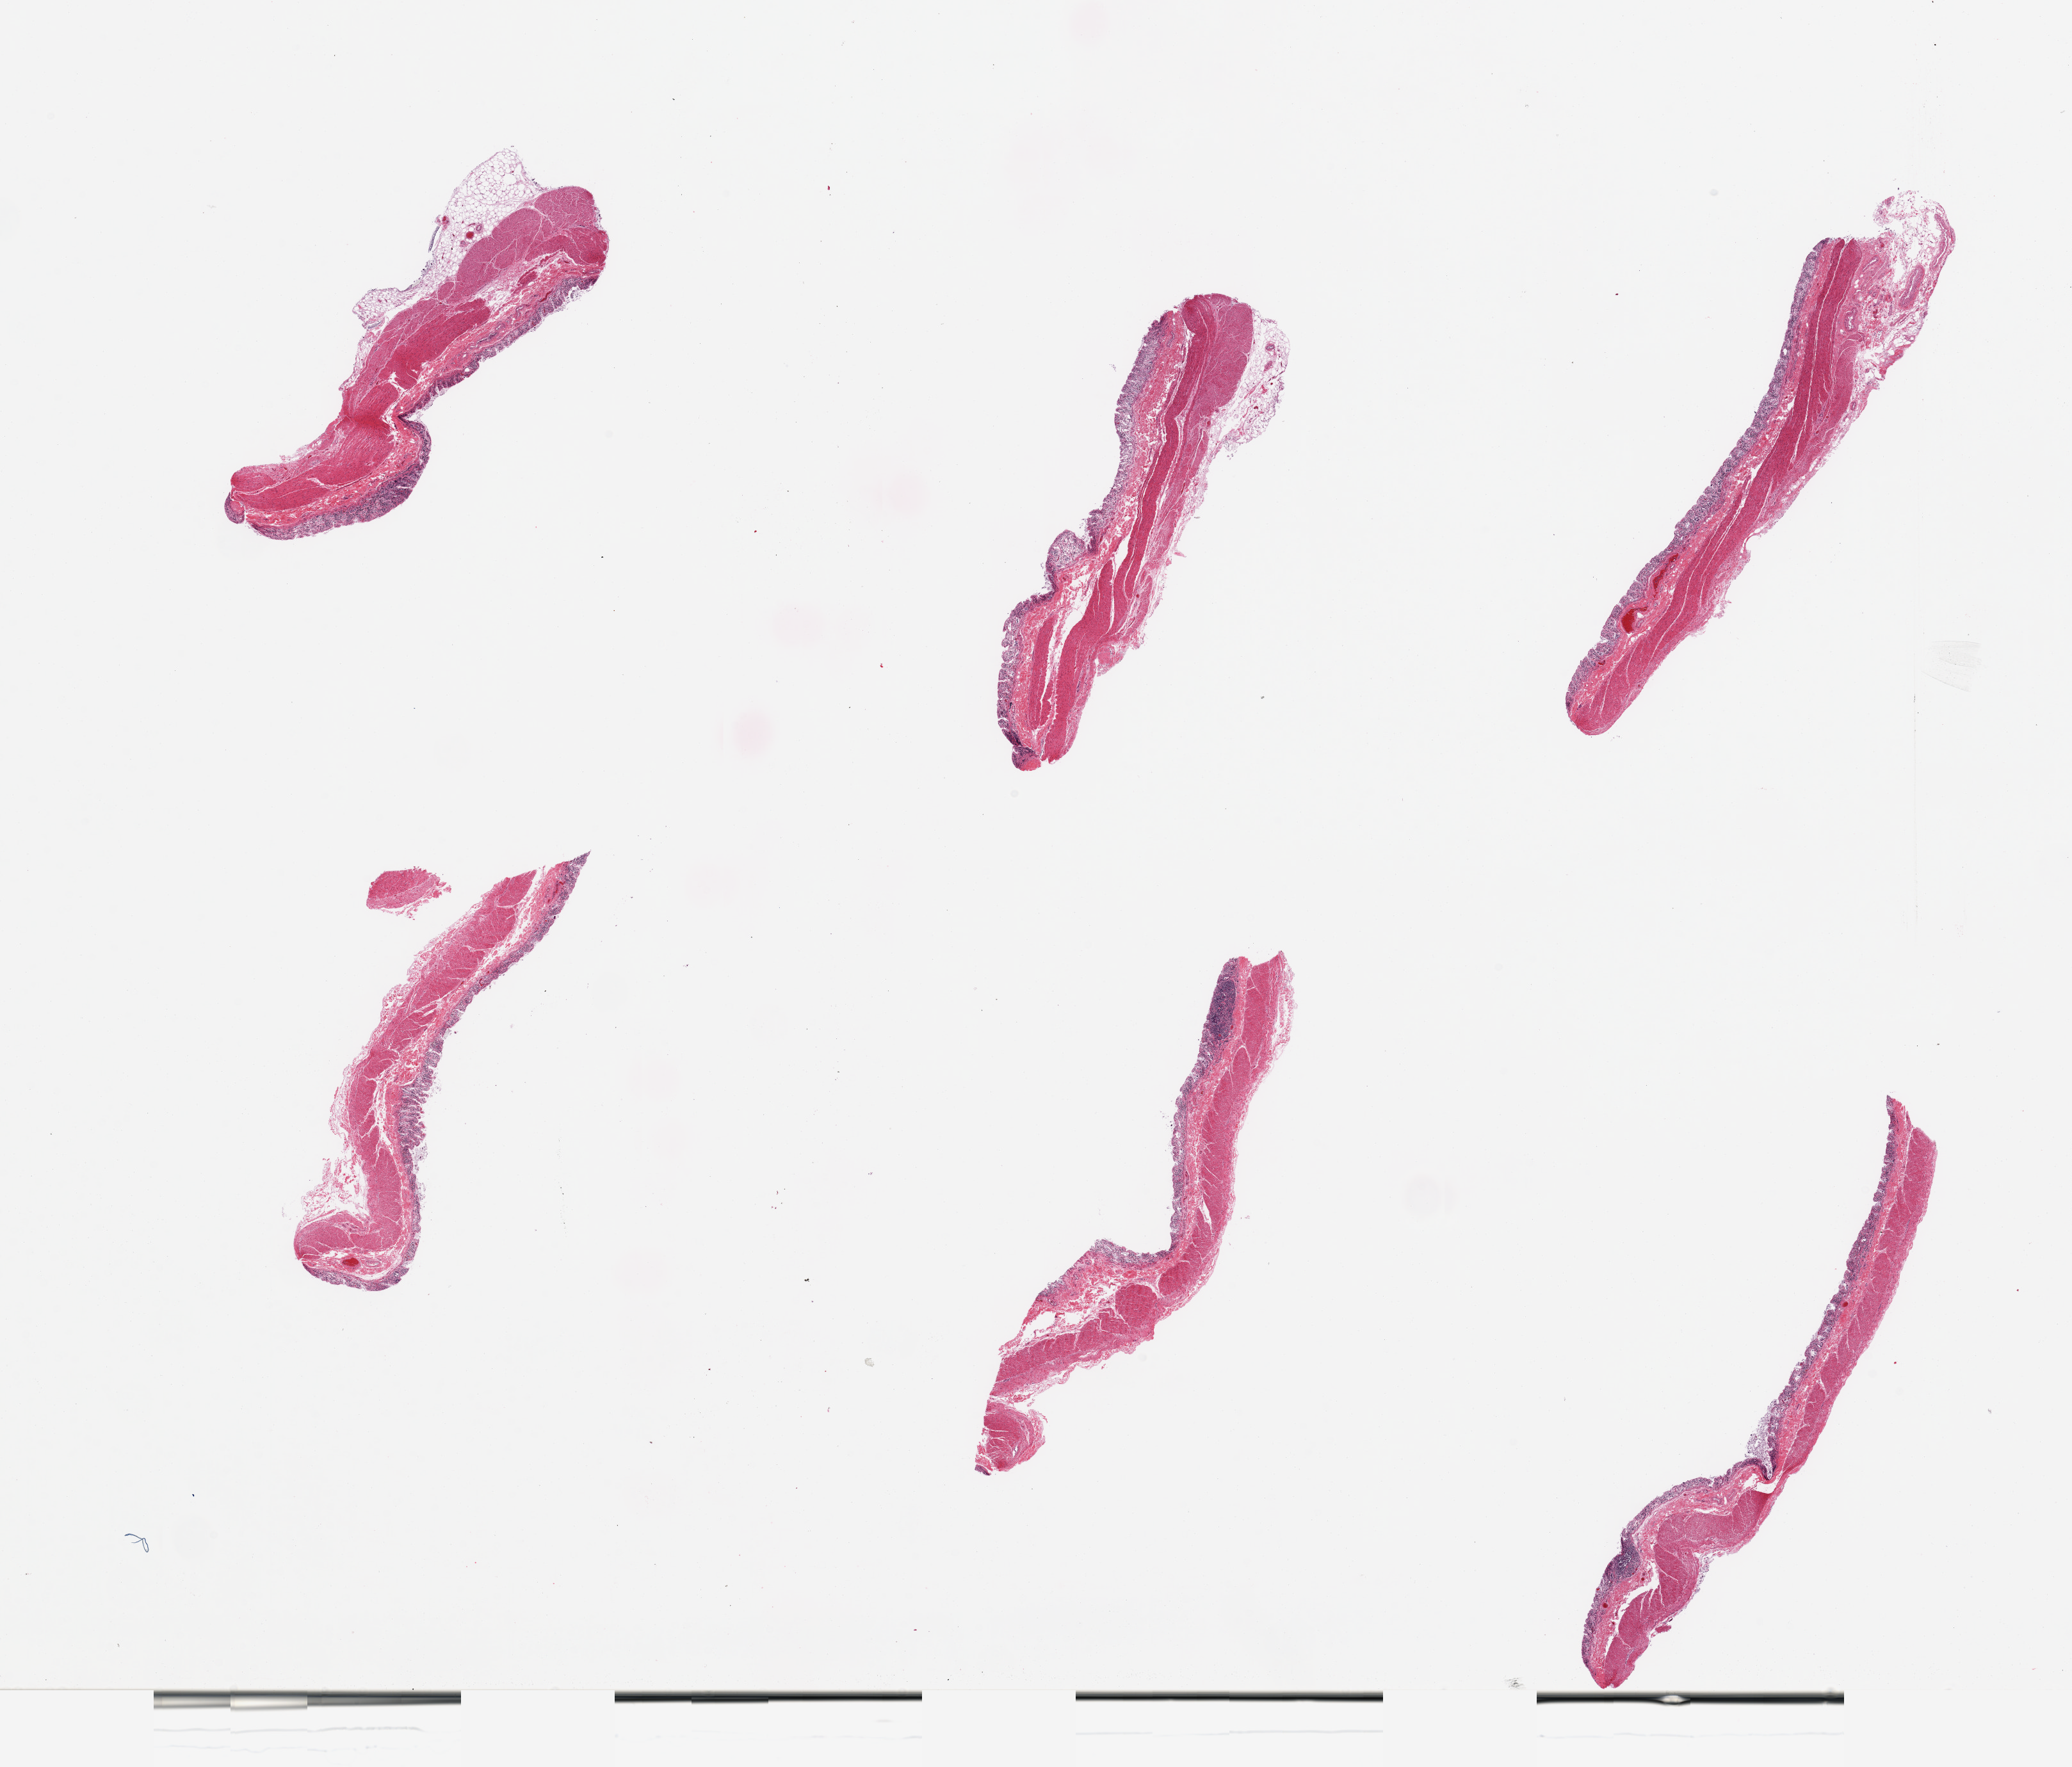
Whole-slide image, hematoxylin and eosin (H&E) stain — low-resolution overview of the scanned area, about 25.6 x 21.8 mm. PAXgene-fixed paraffin-embedded (PFPE) section. Section of transverse colon (target tissue). Tissue donor sample. Donor sex: male.
Reviewer comment on this tissue sample: 6 pieces; mucosa severely autolyzed, muscle intact.